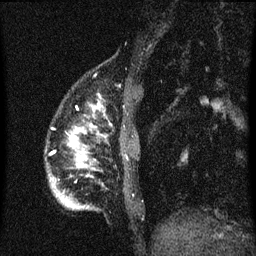
Breast MRI (dynamic contrast-enhanced), one sagittal slice. Position 12 of 60 along the scan axis. Dynamic contrast-enhanced series, image 2 of 3 at this slice position (ordered by acquisition). 1.5 T. TE 4.2 ms, TR 8.4 ms. 2 mm slice thickness. 256 × 256 image matrix, field of view 180 × 180 mm. Patient: female, 34 years. From the clinical record (not read from this slice): setting: breast cancer imaged before/during neoadjuvant chemotherapy; receptor status: HR-positive, HER2-negative.
Structures marked on this image (semi-automatically segmented with operator editing):
- analysis volume of interest (the breast-tissue region the enhancement analysis was run in; not a lesion): bounding box [x1, y1, x2, y2] px = [46, 94, 137, 211]
- tumour enhancement mask (voxels above the 70 % enhancement threshold inside the analysis volume of interest): [70, 130, 85, 167]